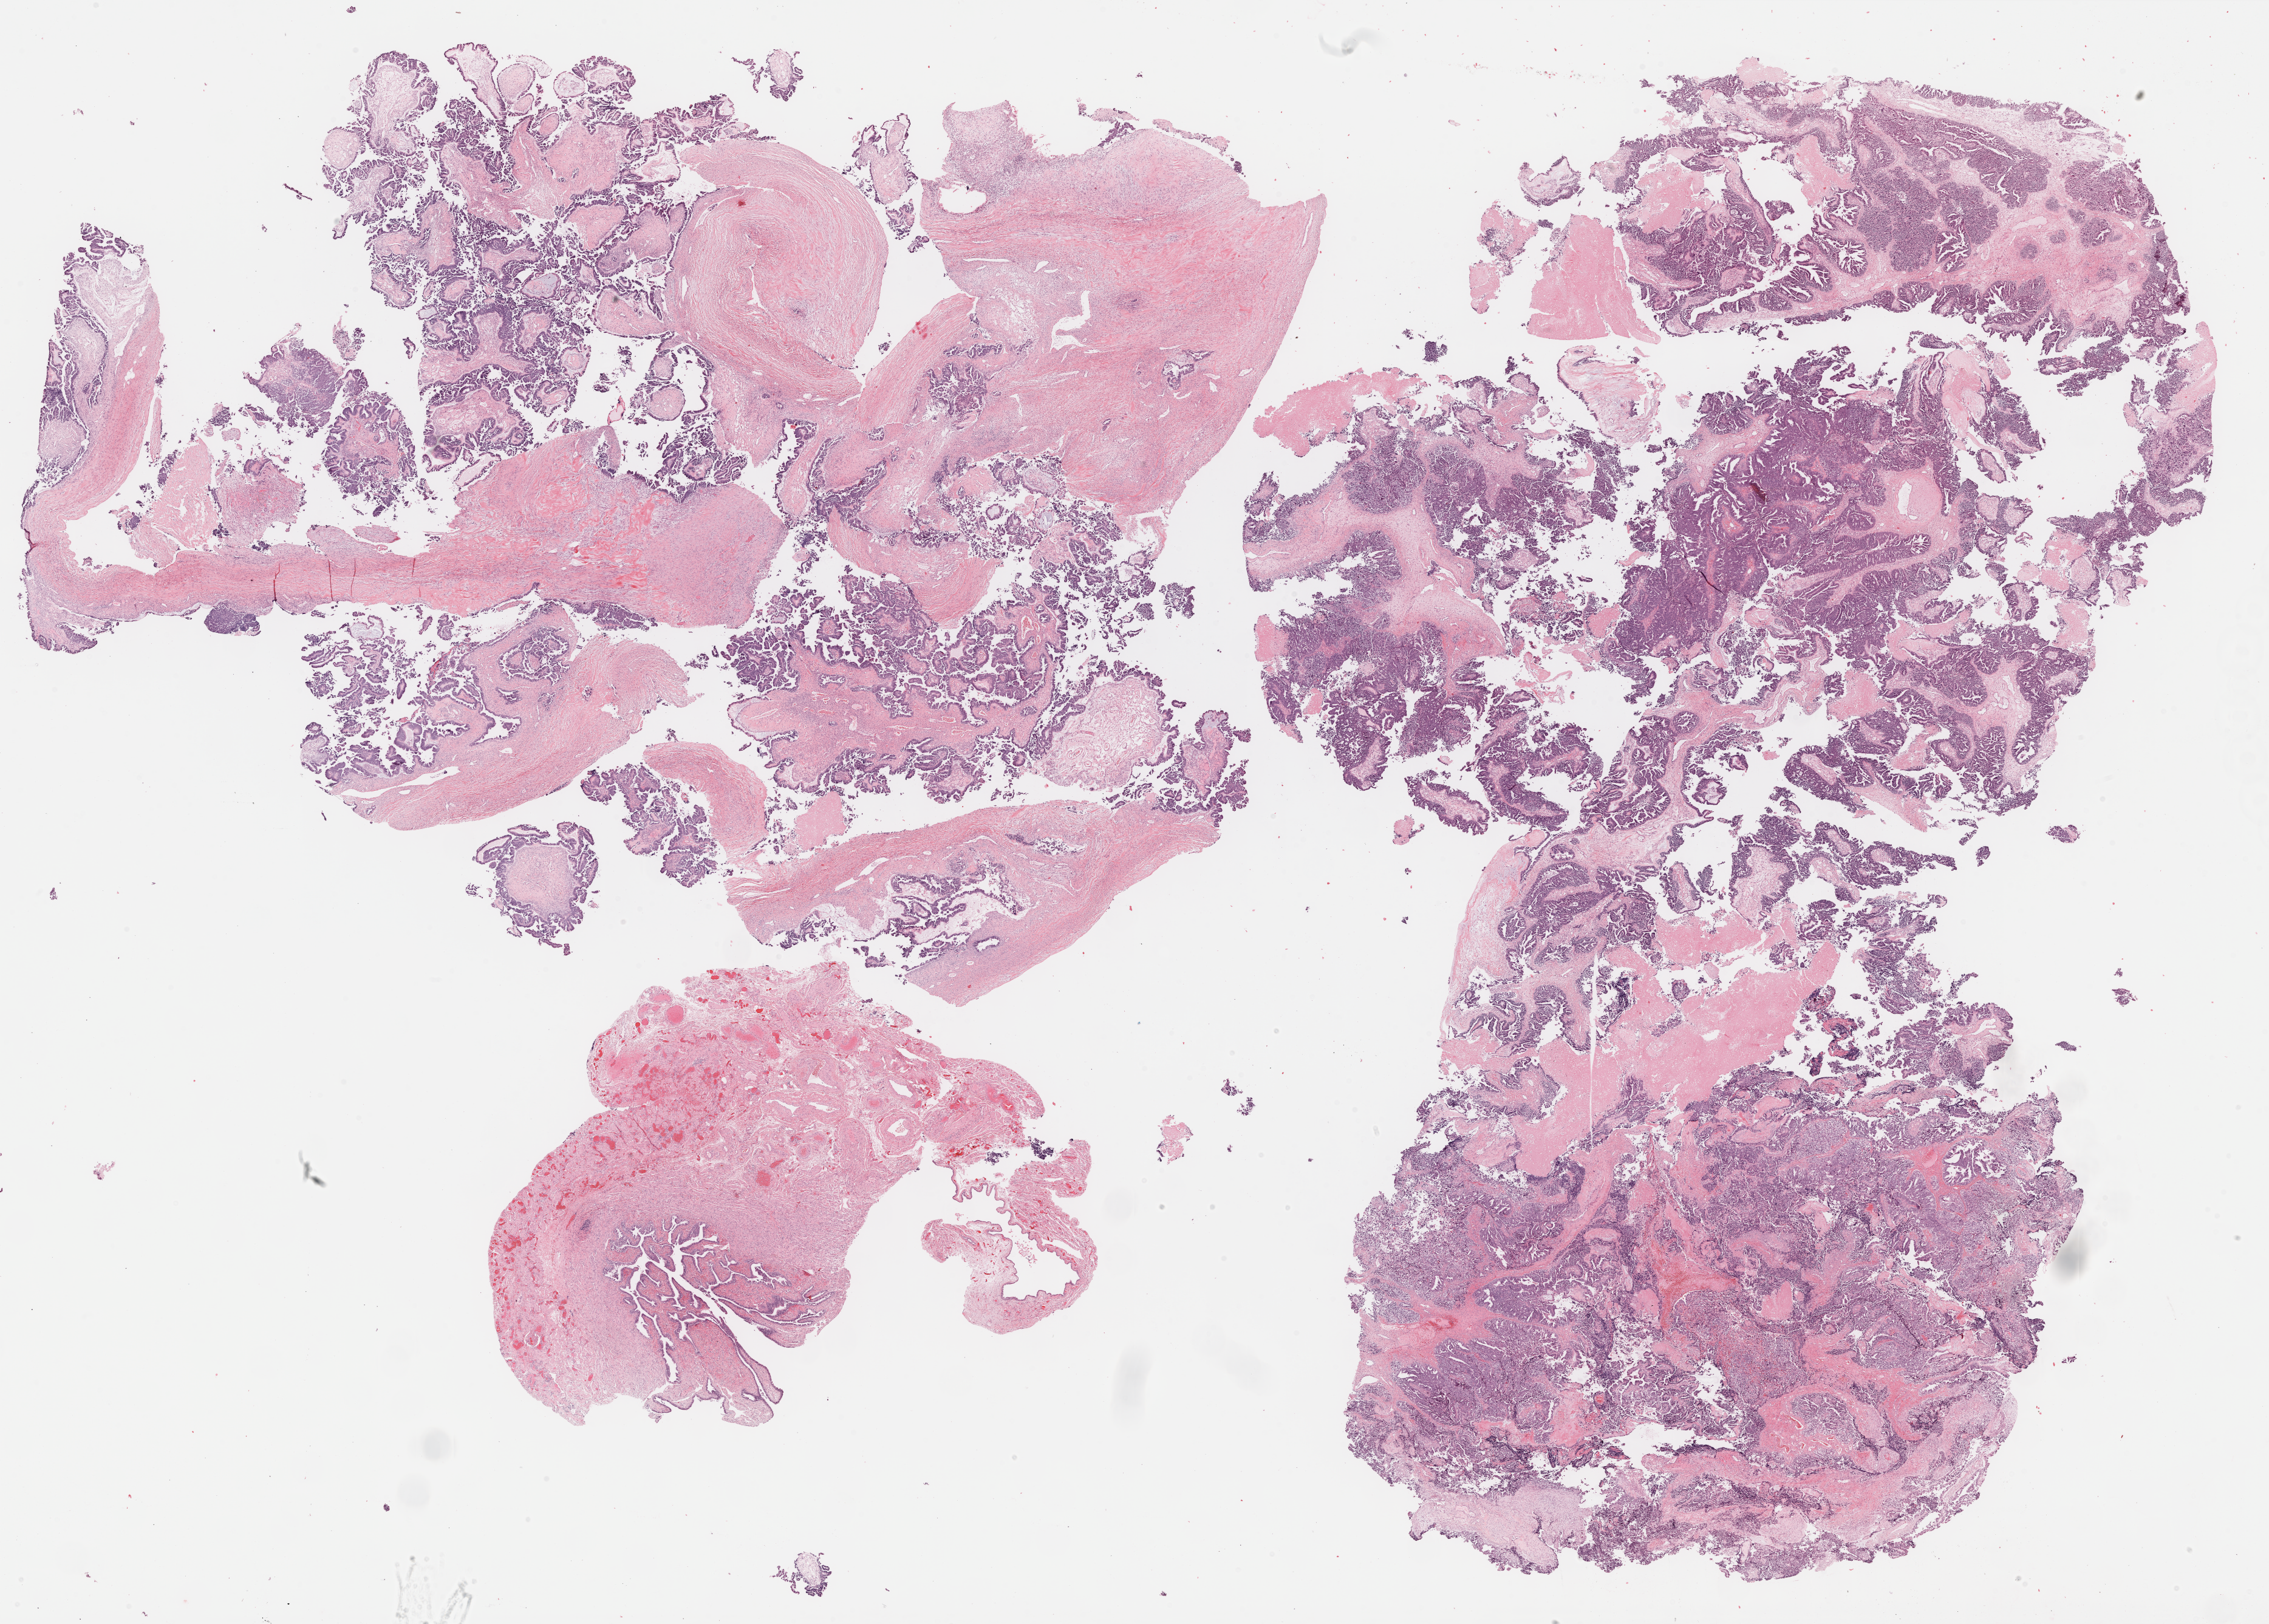
Whole-slide histology image, H&E-stained, whole scanned area (about 30.2 x 21.6 mm, acquisition: 40x scan) shown as a low-resolution overview. FFPE section. Sample: primary tumour, ovary. Female patient; age at initial diagnosis 70 years. Histologic grade: G3 (poorly differentiated).
• histologic diagnosis: Serous cystadenocarcinoma, NOS
• FIGO stage: IIIC
• laterality: bilateral